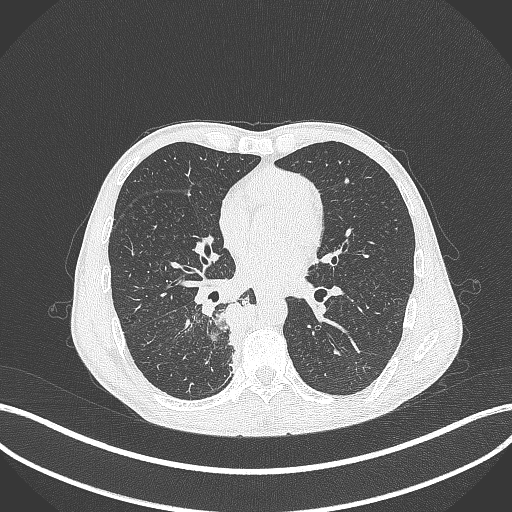
Chest CT, one axial slice; position 178 of 371 along the scan axis; 120 kVp; lung window (W 1500 / L -600 HU); 1 mm slice thickness; 512 × 512 image matrix, field of view 400 × 400 mm. Patient: male, 58 years. Case-level facts recorded for this patient, not image findings: clinical TNM (as recorded): T3 N1 M1.
Structures marked on this image (rectangle marked by the reading radiologist):
- lung tumour (recorded histology: squamous cell carcinoma): bounding box <217,295,270,370> (left, top, right, bottom; pixels)